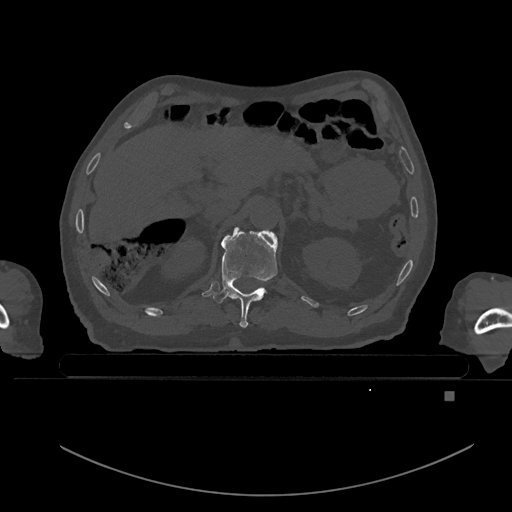
CT including the spine, one axial slice. Slice 19 of 969 in the series (ordered by position). Bone window (W 1800 / L 400 HU). 512 × 512 image matrix, field of view 456 × 456 mm. Male patient, age 82 years. Case-level facts recorded for this patient, not image findings: primary cancer: prostate; vertebrae with lytic lesions (as recorded): T11, T9, T8, T2.
Outlined on this slice (semi-automatic segmentation, software-assisted and operator-edited):
- T11 vertebra: box from (x=213, y=229) to (x=278, y=328) px